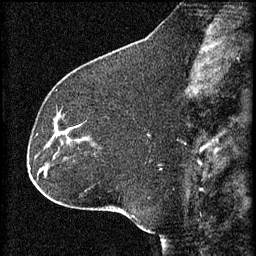
Breast MRI (dynamic contrast-enhanced), one sagittal slice; position 25 of 60 along the scan axis; 3 images stored at this slice position (order not interpretable as contrast timing); 1.5 T; TE 4.2 ms, TR 8.2 ms; 2 mm slice thickness; 256 × 256 image matrix, field of view 180 × 180 mm. Female patient, age 32 years.
Structures marked on this image (semi-automatically segmented with operator editing):
- analysis volume of interest (the breast-tissue region the enhancement analysis was run in; not a lesion): bounding box <48,114,84,157> (left, top, right, bottom; pixels)
- tumour enhancement mask (voxels above the 70 % enhancement threshold inside the analysis volume of interest): <54,128,71,141>